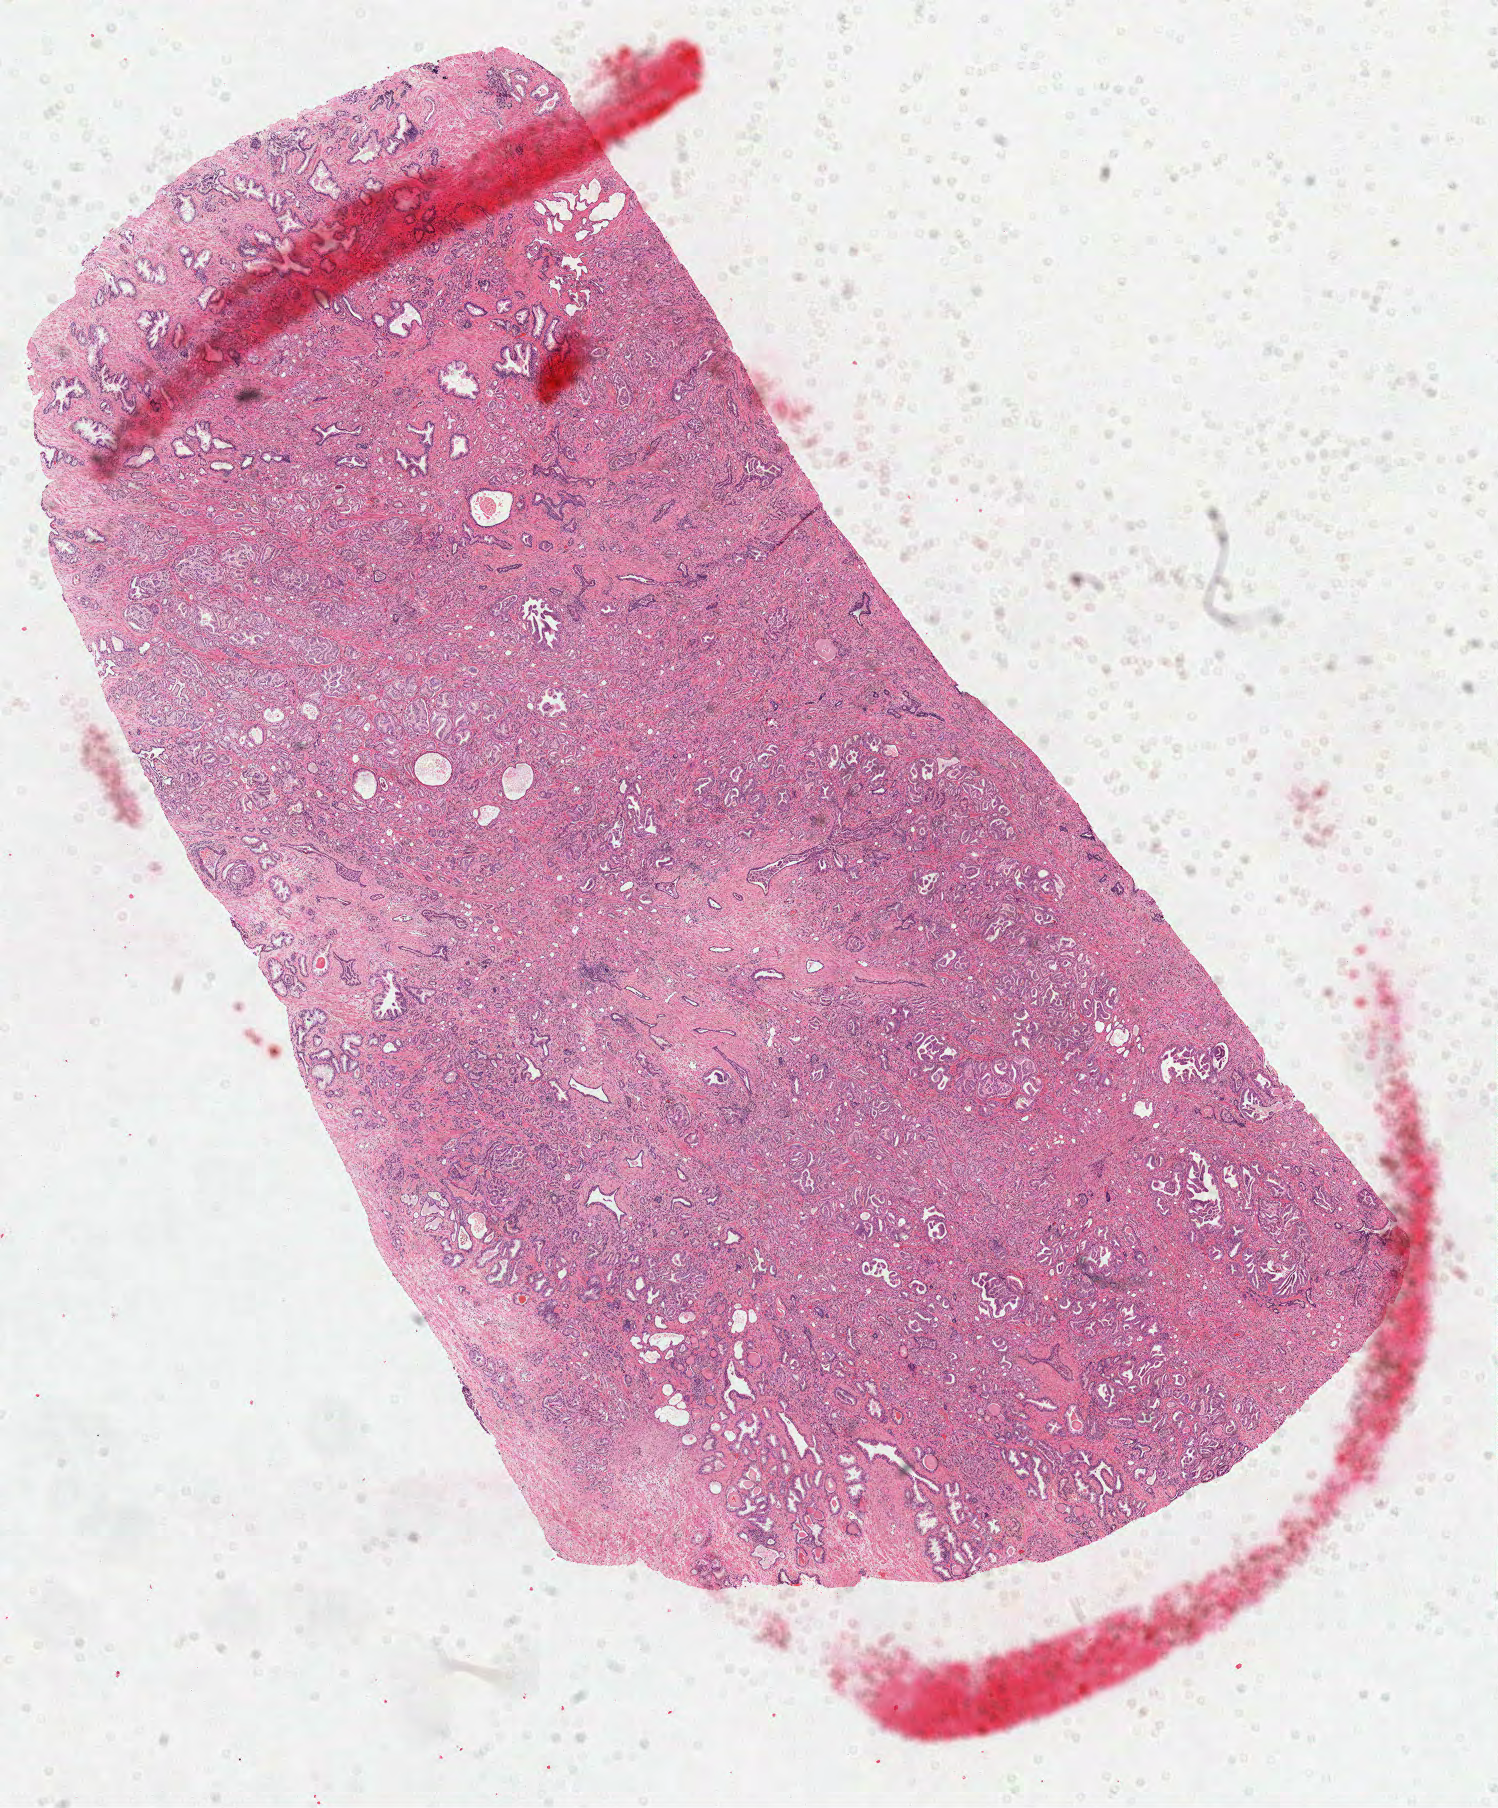
Whole-slide histology image, H&E — whole scanned area (about 12.1 x 14.6 mm, slide scanned at 40x) shown as a low-resolution overview, formalin-fixed paraffin-embedded (FFPE) diagnostic section, primary tumour sample from the prostate. Patient: male, age at initial diagnosis 52 years. Gleason score: 7 (4+3).
• laterality: bilateral
• lymph nodes positive (case pathology): 0 of 4 examined
• pathologic diagnosis: Acinar cell carcinoma